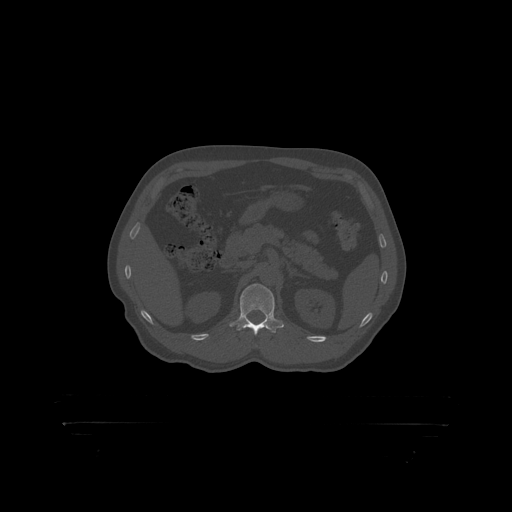
CT including the spine, one axial slice. Reconstruction kernel STANDARD. 120 kVp. Bone window (W 1800 / L 400 HU). 512 × 512 image matrix. Patient: male, 46 years. Case-level facts recorded for this patient, not image findings: primary cancer: skin.
Outlined on this slice (semi-automatically segmented with operator editing):
- L1 vertebra: box from (x=240, y=284) to (x=275, y=319) px